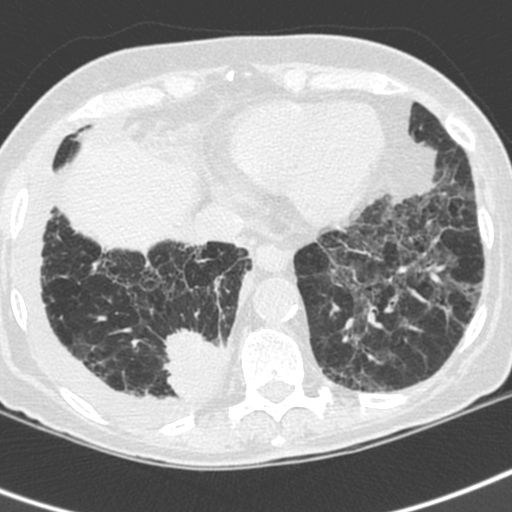
Low-dose screening chest CT, axial slice; baseline annual screen; lung window (W 1500 / L -600 HU); slice 145 of 192 in the series; 512 × 512 image matrix. Female participant, aged 73 years at enrolment. Current smoker at enrolment.
• Expert reader's lesion annotation, box from (x=158, y=321) to (x=235, y=405) px.
• Screening reader's record for this exam (one nodule recorded; not confirmed to be the boxed lesion): non-calcified nodule or mass ≥4 mm, right lower lobe, 35 × 30 mm, spiculated (stellate) margins, soft tissue attenuation.
• Lung cancer was diagnosed 22 days after this screen: adenocarcinoma, NOS, right lower lobe, stage IV (AJCC 6th edition), 35 mm at pathology.